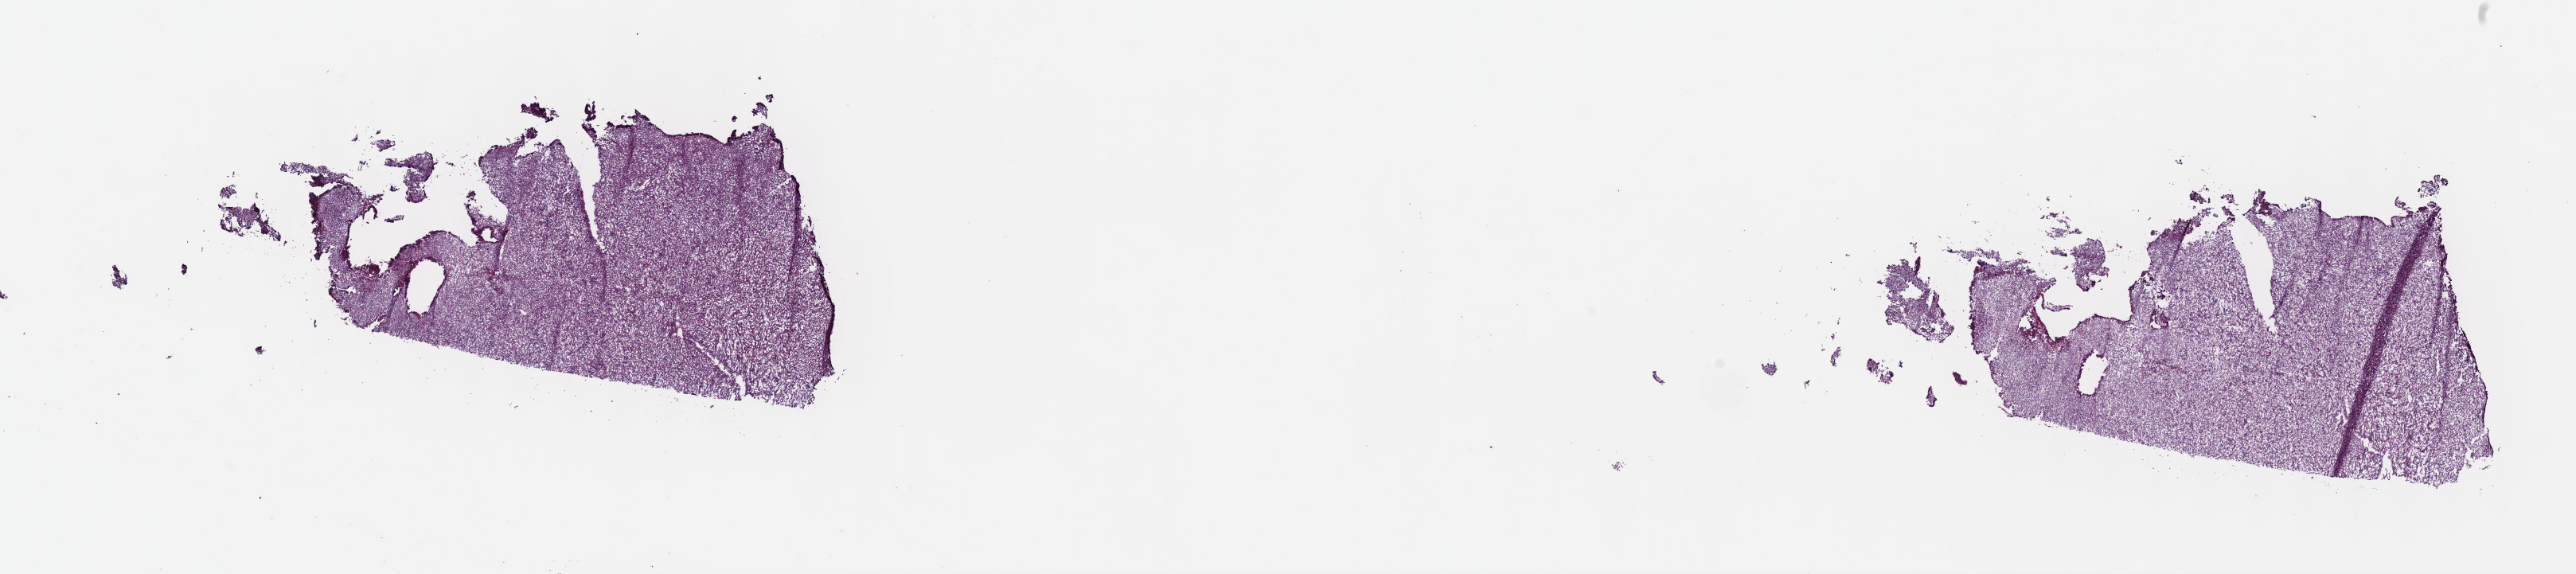
Hematoxylin and eosin (H&E) stained whole-slide image, shown as a low-resolution overview of the whole scanned area (about 26.2 x 5.8 mm), frozen section from the top of the tissue portion, connective, subcutaneous and other soft tissues, primary tumour sample. Patient: male, age at initial diagnosis 69 years. Composition of this section per pathologist review: tumour cells 100%, tumour nuclei 80%, normal cells 0%, stromal cells 0%, necrosis 0%. Infiltration values recorded for this section: lymphocyte infiltration 1%, monocyte infiltration 0%, neutrophil infiltration 0%.
Histologic diagnosis: Synovial sarcoma, spindle cell (connective, subcutaneous and other soft tissues of thorax).